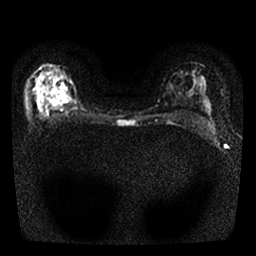
Breast MRI, one axial slice; position 19 of 25 along the scan axis; diffusion-weighted series; image 2 of 4 stored at this slice position (different b-values; order by instance number); 1.5 T; 4 mm slice thickness; 256 × 256 image matrix, field of view 300 × 300 mm. Female patient.
Outlined on this slice (outlined manually by an expert reader):
- tumour on diffusion-weighted imaging: box from (x=39, y=97) to (x=43, y=112) px